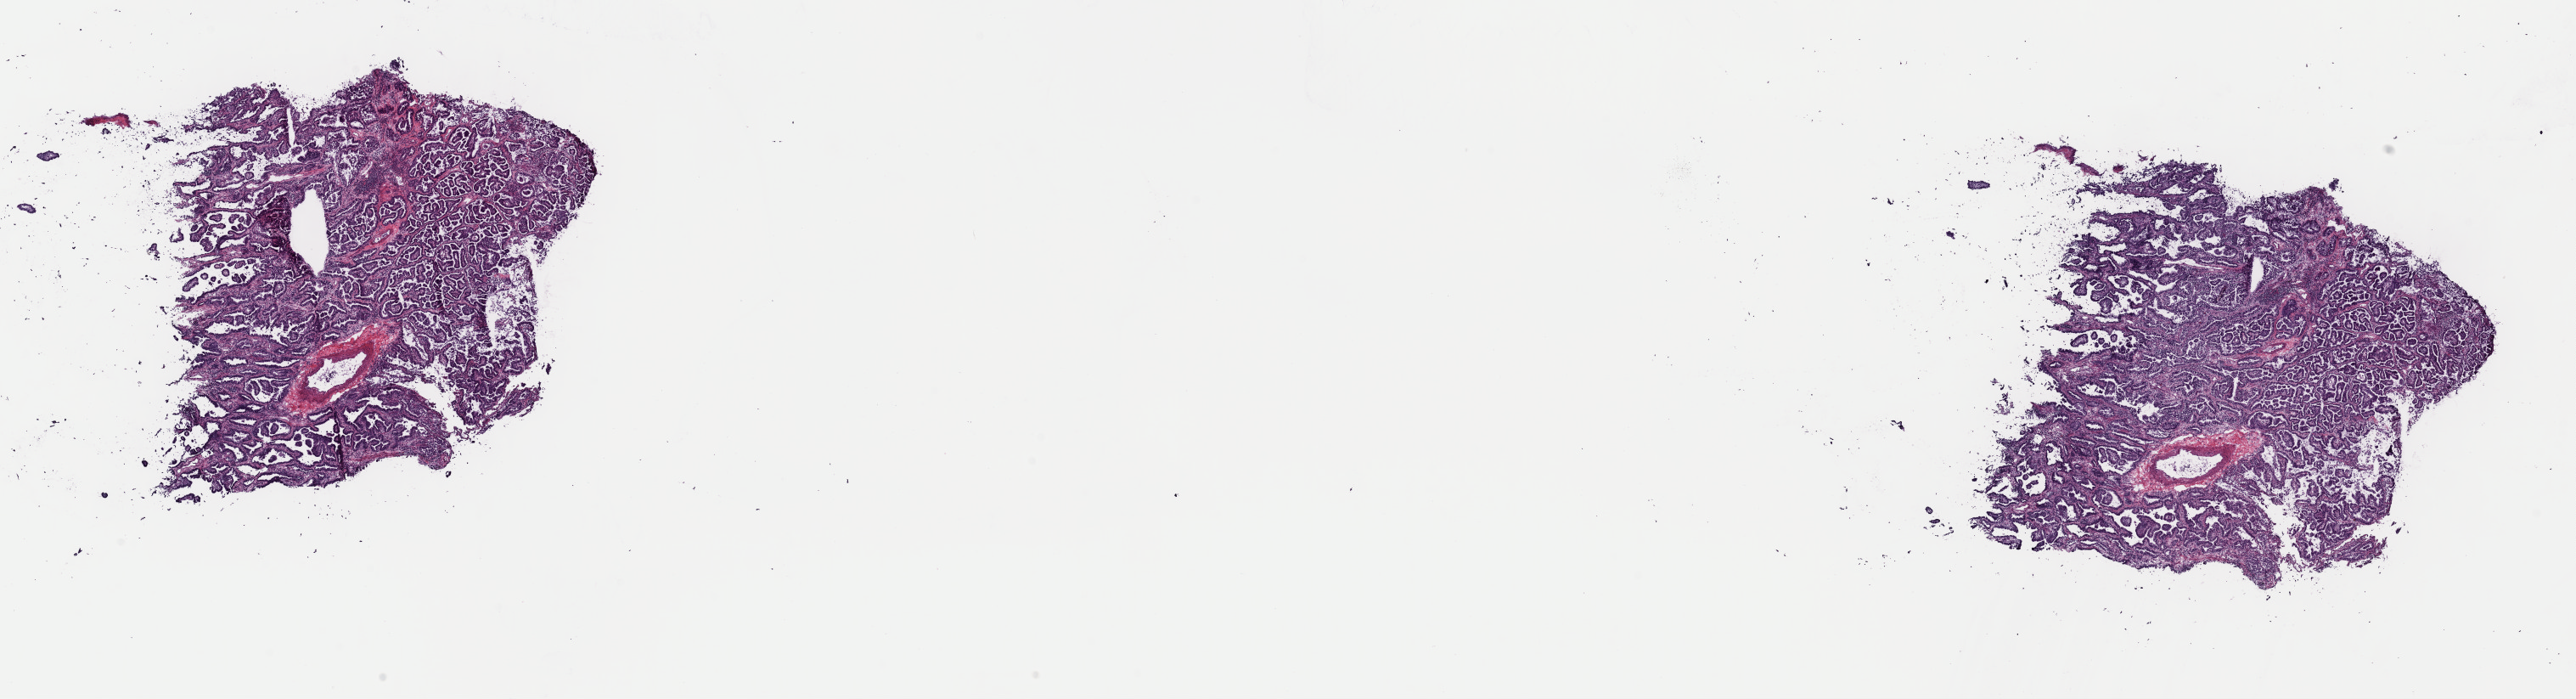
Whole-slide histology image, Hematoxylin and eosin (H&E) stained — whole scanned area (about 24.0 x 6.5 mm, slide scanned at 40x) shown as a low-resolution overview, frozen section from the top of the tissue portion, primary tumour sample from the lung. Female, age 76 years at initial diagnosis. Slide review estimates, as recorded: tumour cells 80%, tumour nuclei 80%, normal cells 5%, stromal cells 5%, necrosis 10%. Infiltration values recorded for this section: lymphocyte infiltration 60%, monocyte infiltration 15%, neutrophil infiltration 5%.
• TNM: T2 N0 M0
• AJCC pathologic stage: IB (6th edition)
• diagnosis: Adenocarcinoma, NOS (upper lobe, lung)